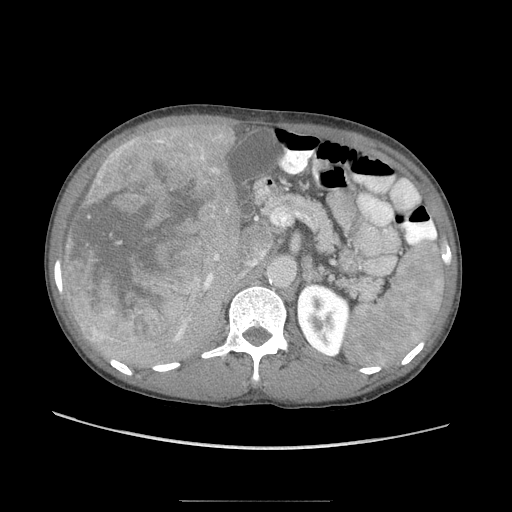
Contrast-enhanced abdominal CT (liver protocol), one axial slice; position 46 of 103 along the scan axis; 120 kVp; soft-tissue window (W 400 / L 40 HU); 512 × 512 image matrix. Case-level facts recorded for this patient, not image findings: diagnosis: hepatocellular carcinoma (patient treated with transarterial chemoembolisation; whether this scan precedes or follows treatment is not stated here); TNM stage (as recorded): Stage-IIIA; Child-Pugh class: A; tumour differentiation: moderately differentiated; tumour nodularity: multinodular.
Outlined on this slice (semi-automatically segmented with operator editing):
- liver parenchyma outside the tumour (the mass and vessels are separate outlines, so this box may not span the whole liver): box from (x=64, y=116) to (x=249, y=365) px
- mass: (x=61, y=127)–(x=220, y=347)
- liver vessels: (x=193, y=250)–(x=224, y=304)